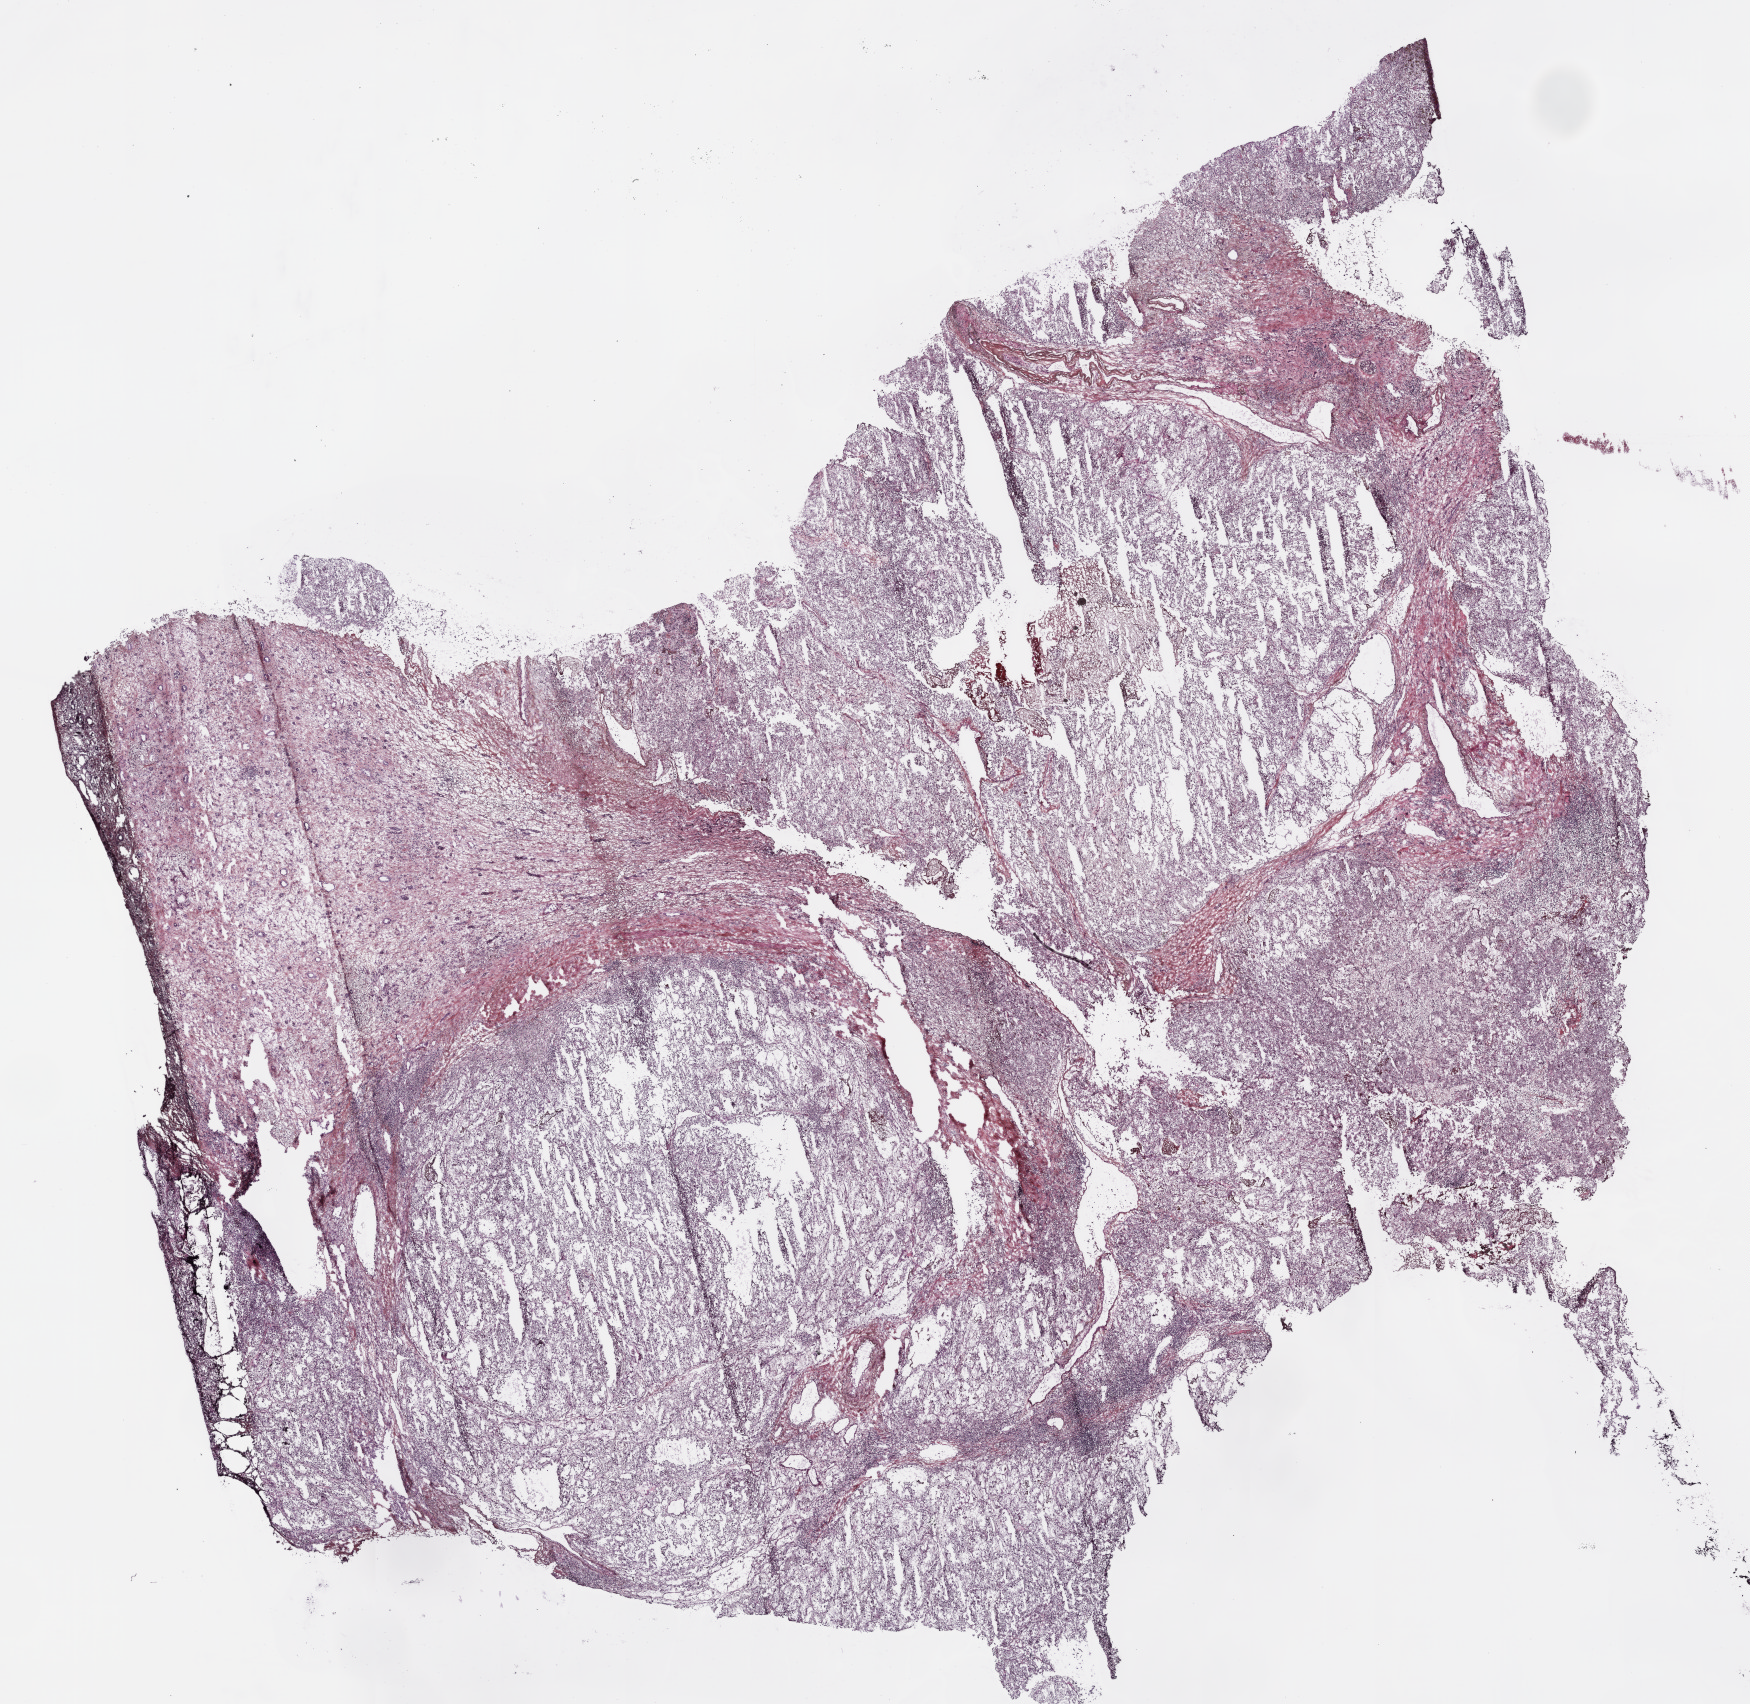
Whole-slide histology image, H&E-stained, whole scanned area (about 14.0 x 13.7 mm) shown as a low-resolution overview. Frozen section. Kidney, primary tumour sample. Male patient; age at initial diagnosis 67 years. Histologic grade: G2 (moderately differentiated). Pathologist review of this section (percent, as recorded): tumour cells 72%, tumour nuclei 75%, normal cells 18%, stromal cells 10%, necrosis 0%.
AJCC pathologic stage: III (6th edition). Histologic diagnosis: Clear cell adenocarcinoma, NOS.